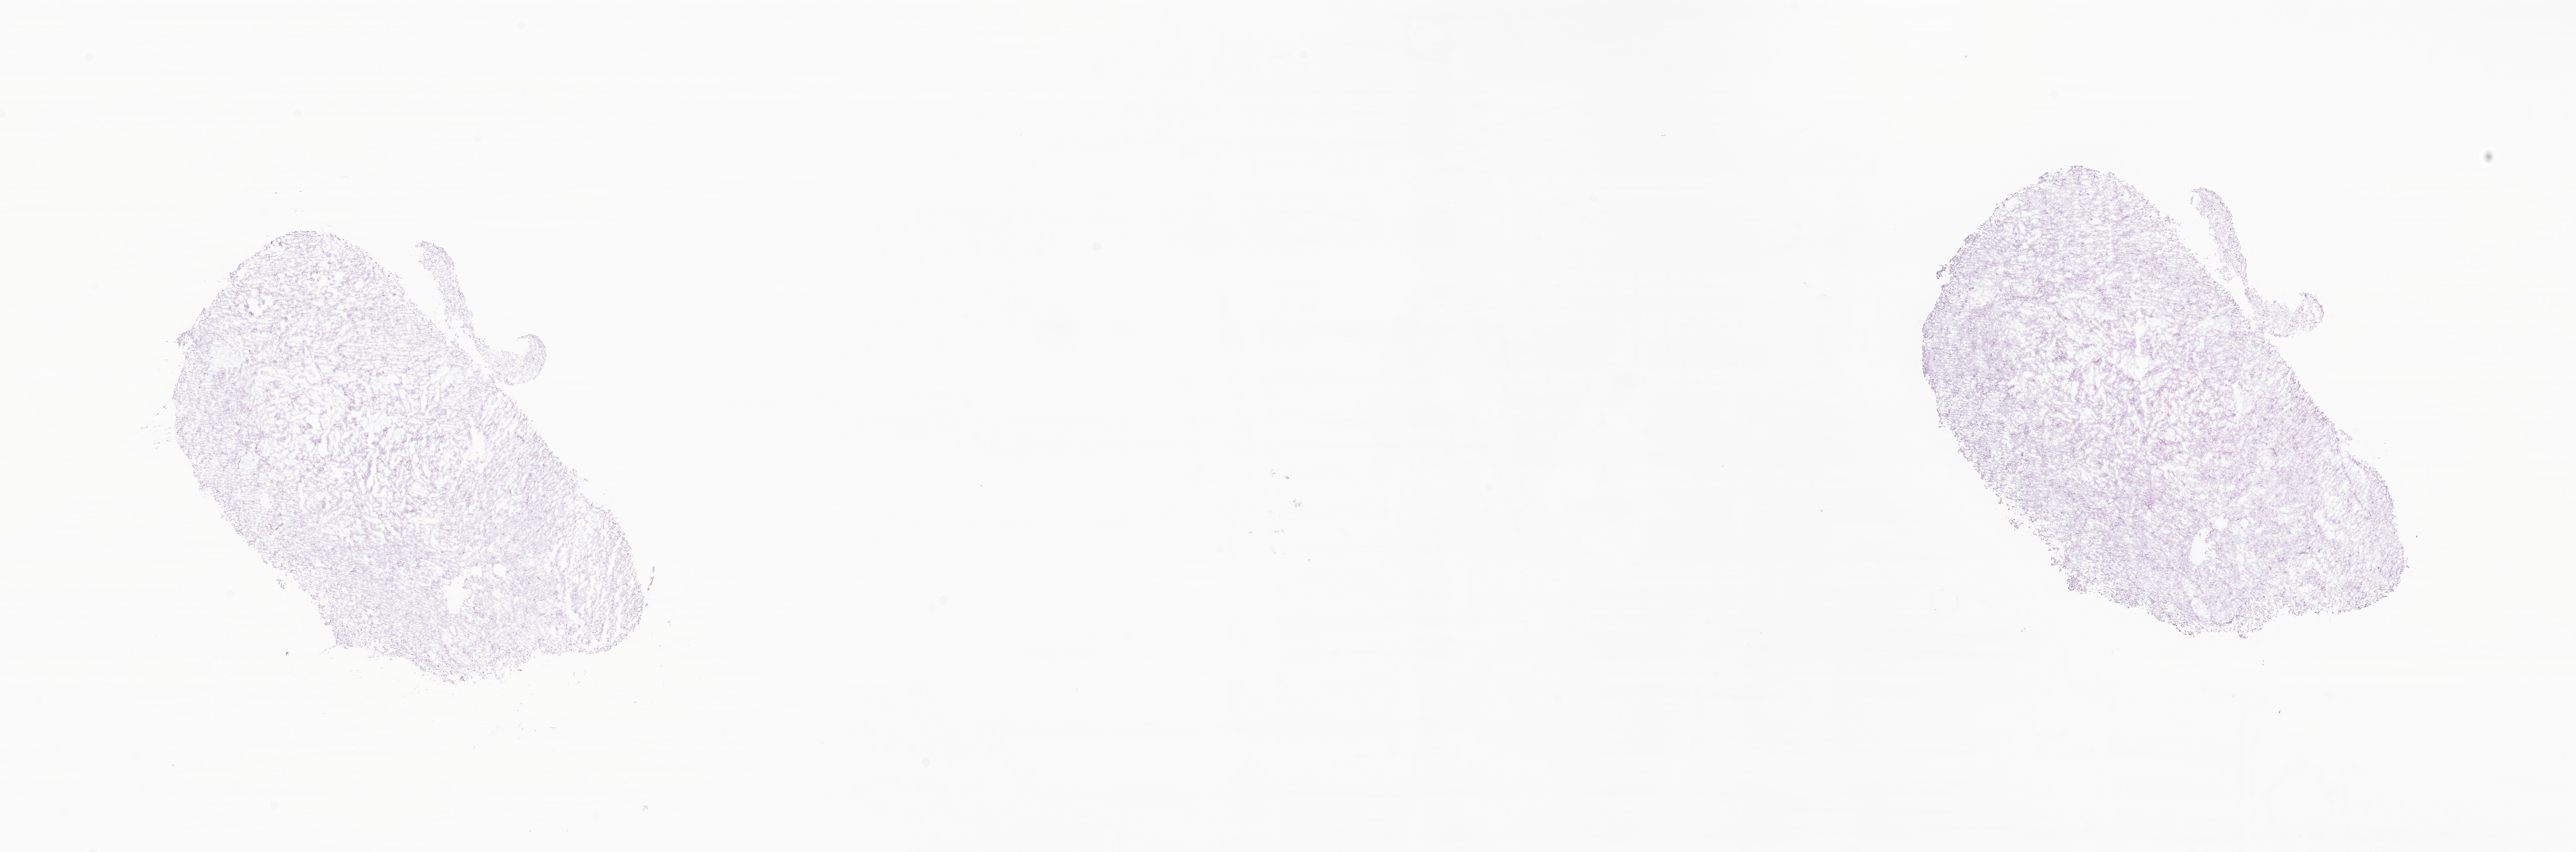
Digitized H&E-stained section of tumor tissue from the brain, whole scanned area (about 28.4 x 9.4 mm) shown as a low-resolution overview; cryosection (OCT / tissue freezing medium). Patient female; age 195 months (16 years 3 months).
Diagnosis: Dysembryoplastic neuroepithelial tumor.